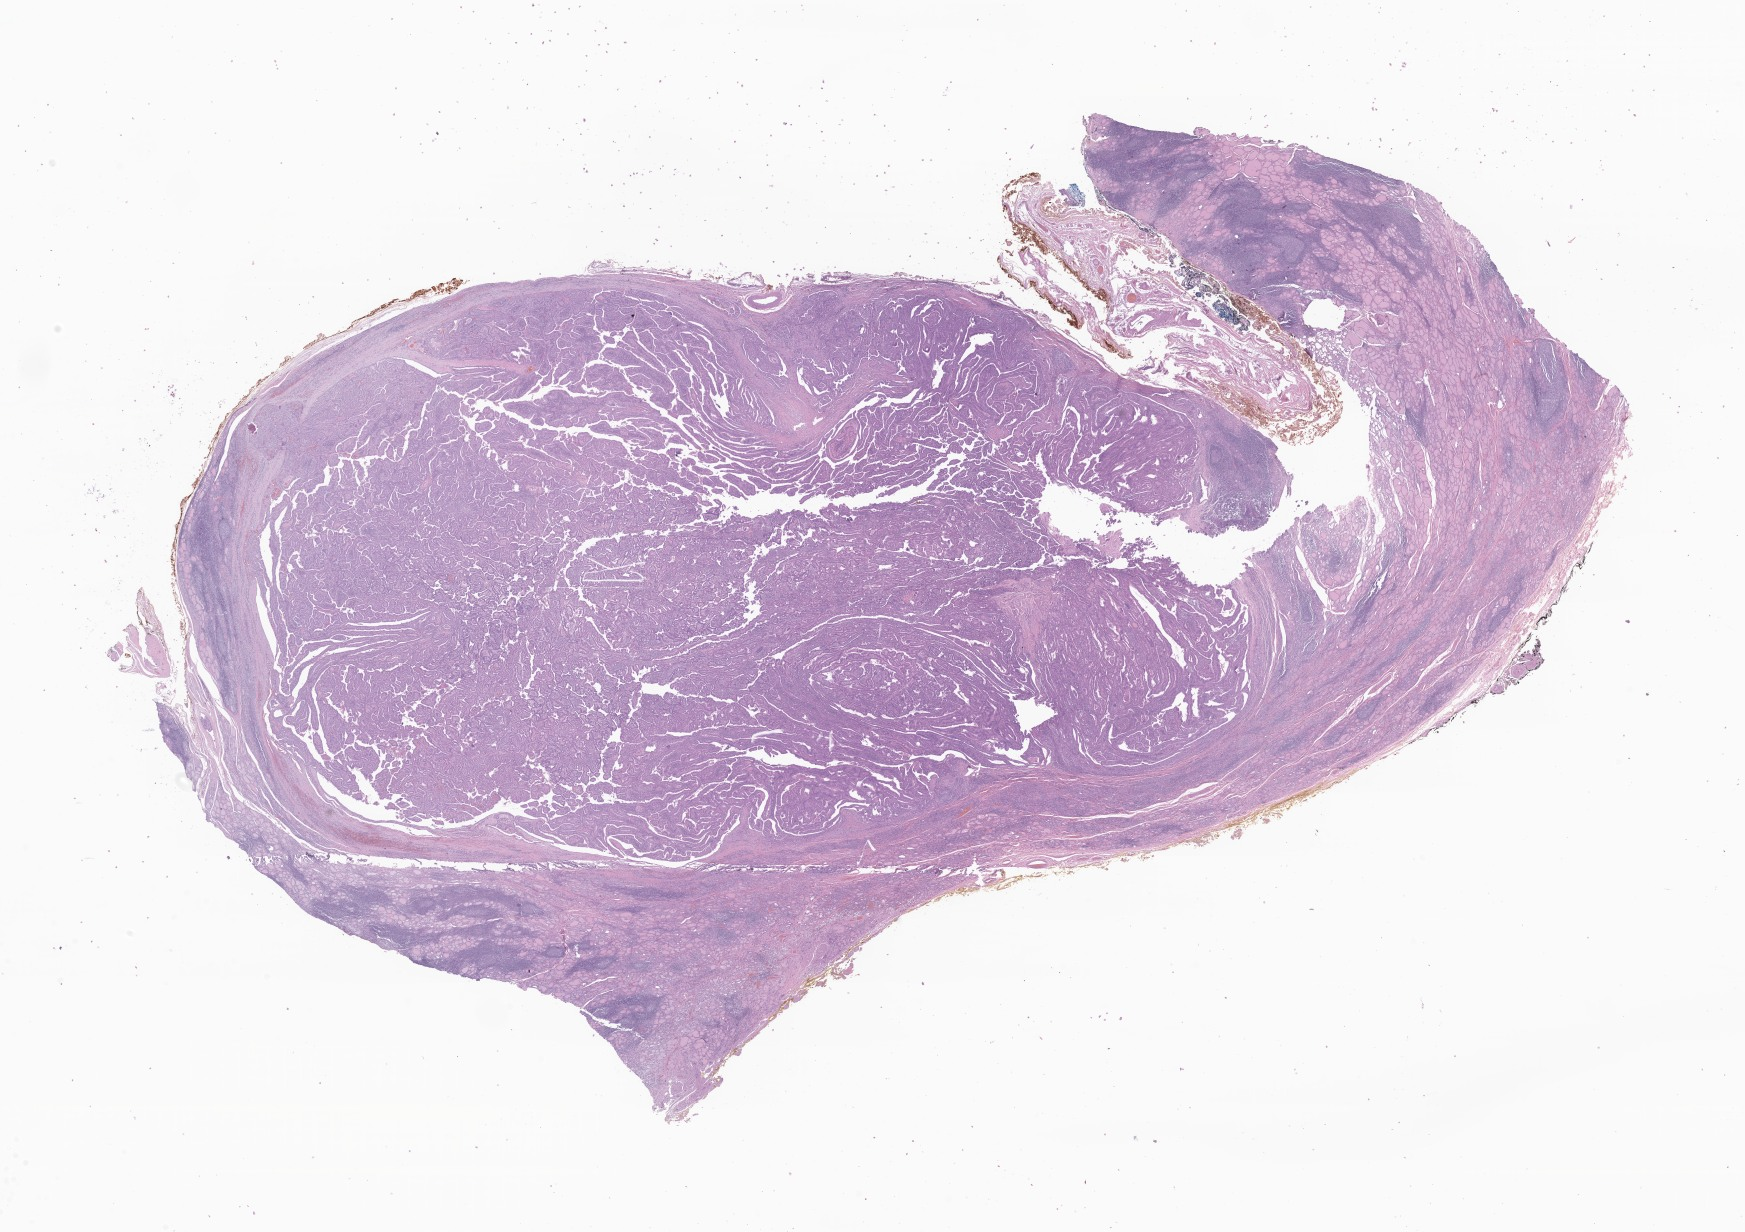
Digitized hematoxylin and eosin (H&E)-stained section of tumor tissue from the thyroid, a low-resolution overview of the entire scanned area, about 29.4 x 20.8 mm; formalin-fixed, paraffin-embedded (FFPE) tissue. Patient: female, age 183 months (15 years 3 months).
Diagnosis (ICD-O-3 morphology term): Papillary adenocarcinoma, NOS.